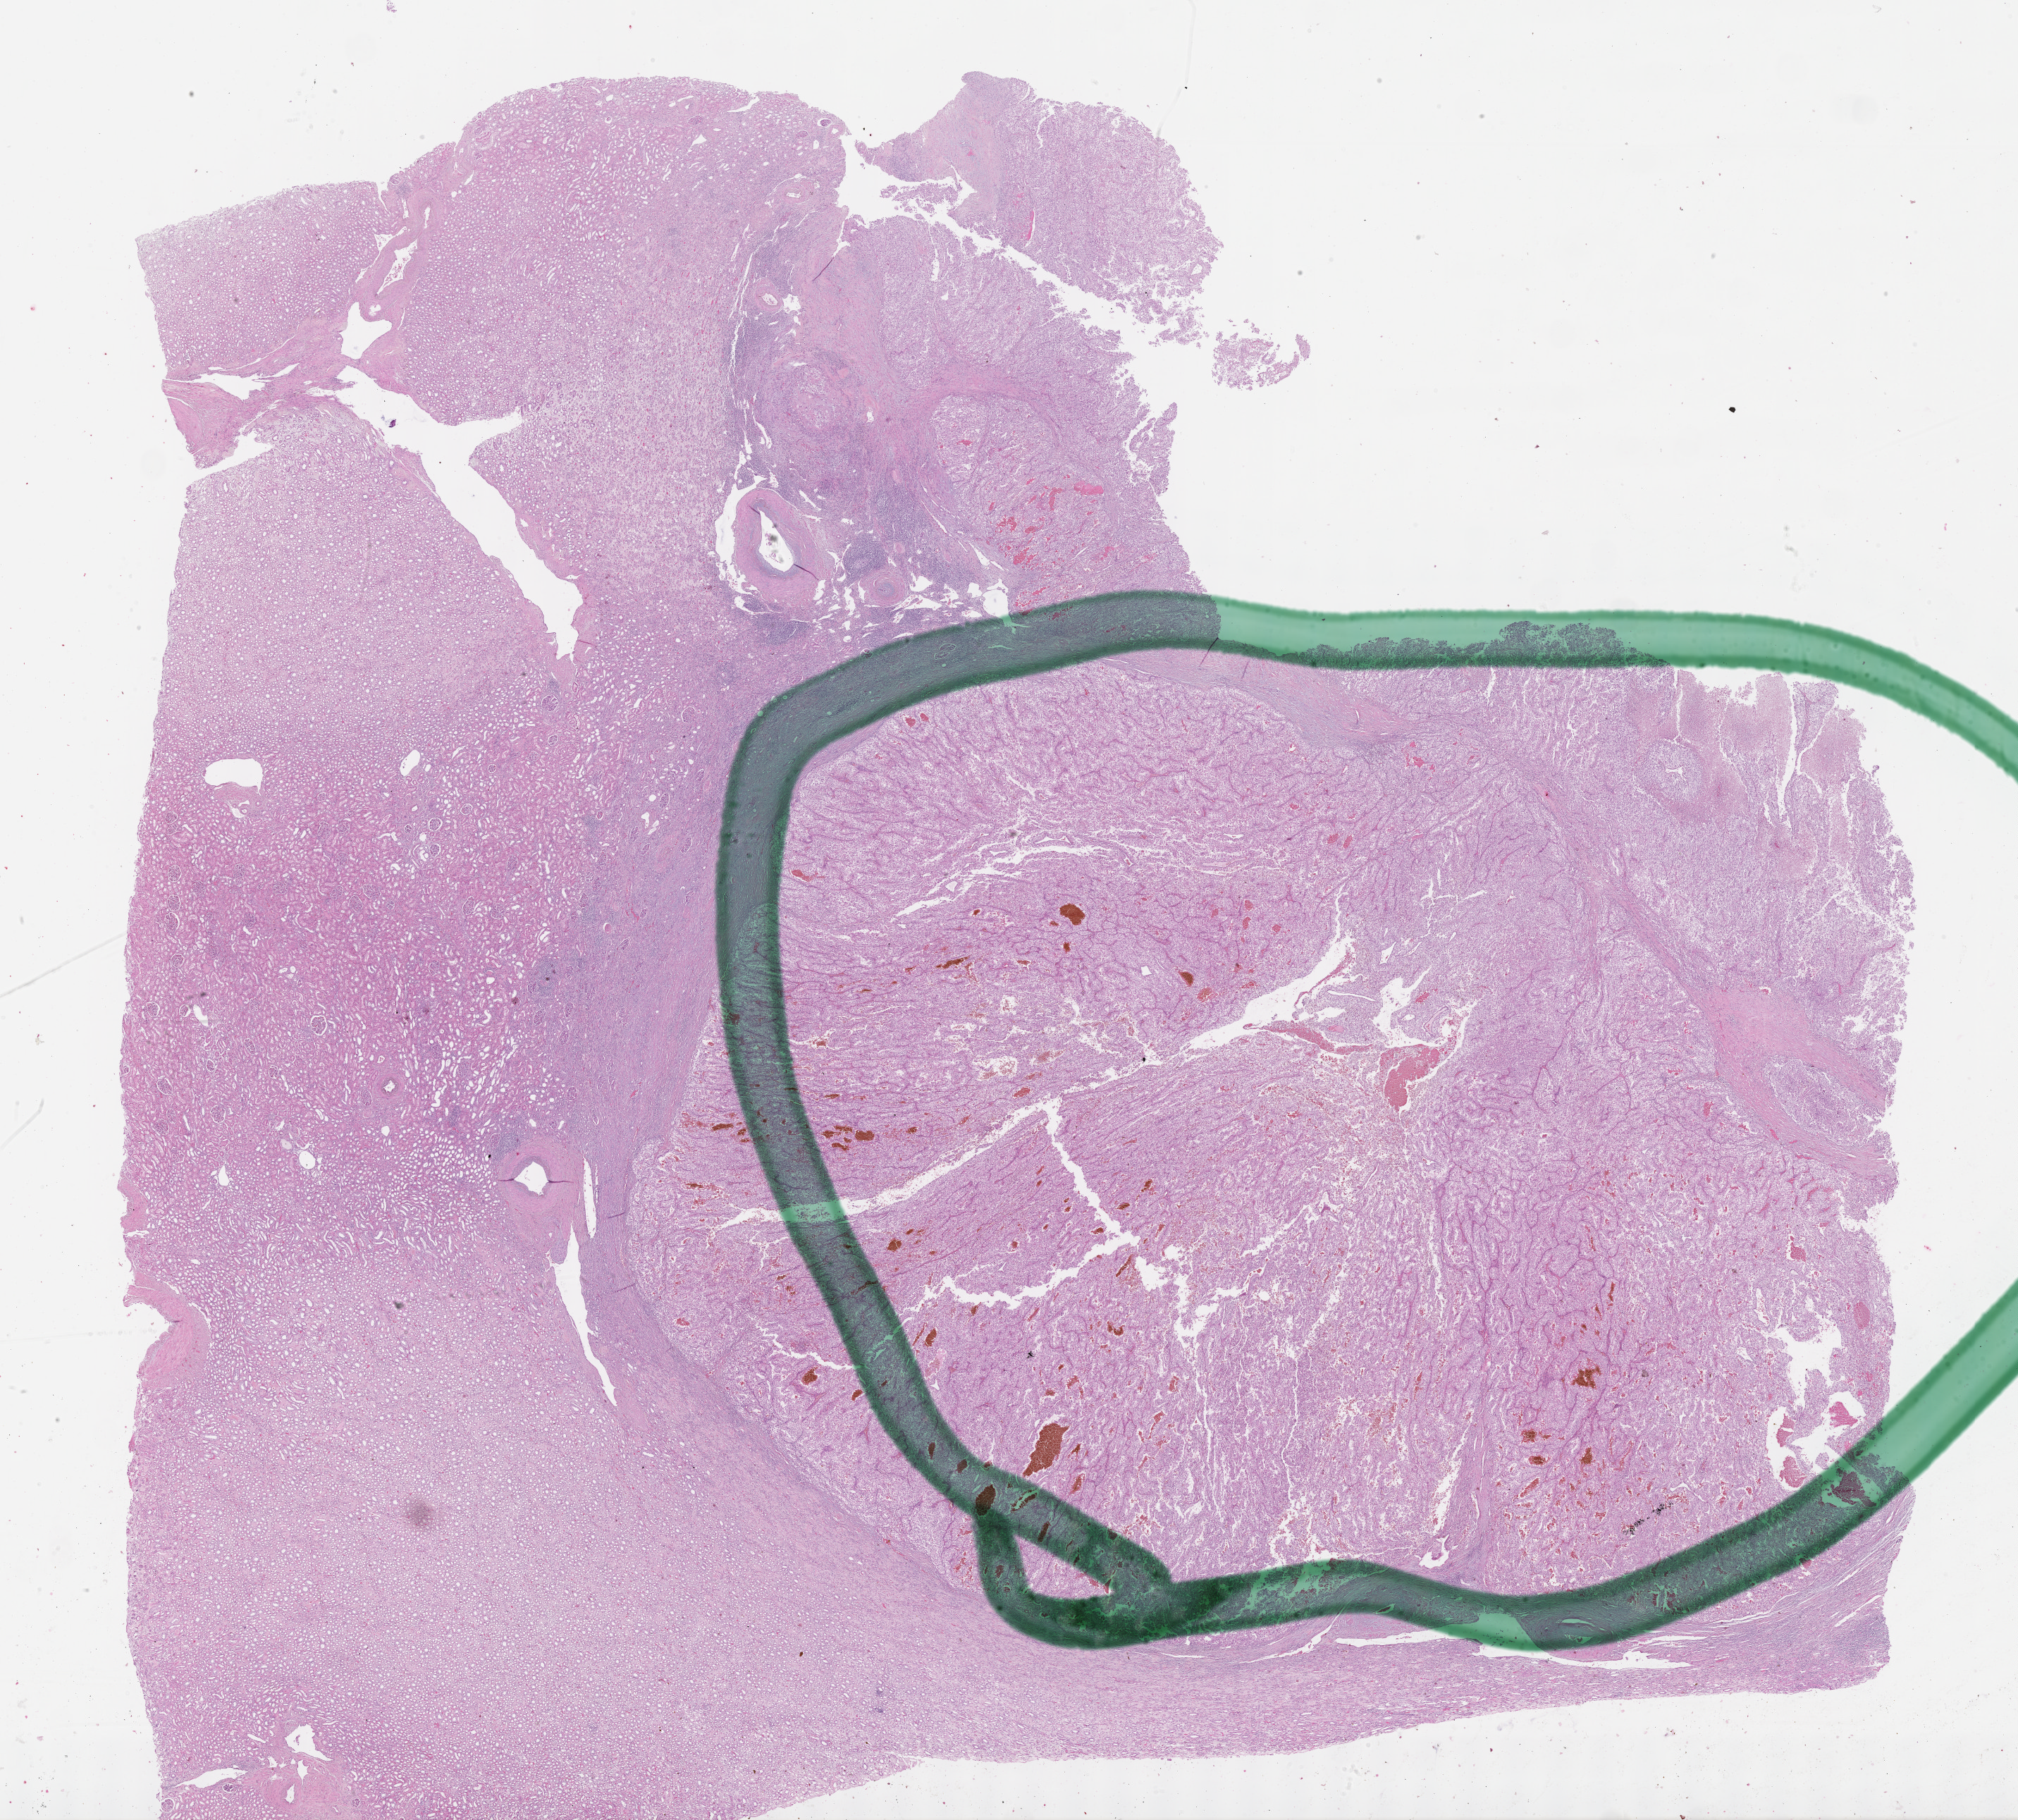
H&E whole-slide image — whole scanned area (about 23.1 x 20.9 mm, slide scanned at 40x) shown as a low-resolution overview. FFPE section. Primary tumour sample from the kidney. Male patient; age at initial diagnosis 77 years.
Pathologic diagnosis: Clear cell adenocarcinoma, NOS.